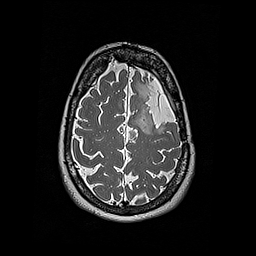
Brain MRI from a brain-tumour surgery series, one axial slice; position 139 of 192 along the scan axis; 1 mm slice thickness; 256 × 256 image matrix, field of view 250 × 250 mm. From the clinical record (not read from this slice): histopathology: Oligodendroglioma; WHO grade: 2; IDH mutation: yes; tumour location: Left Frontal.
Annotated regions visible in this slice (manually delineated by an expert):
- tumour: bounding box <144,114,156,134> (left, top, right, bottom; pixels)